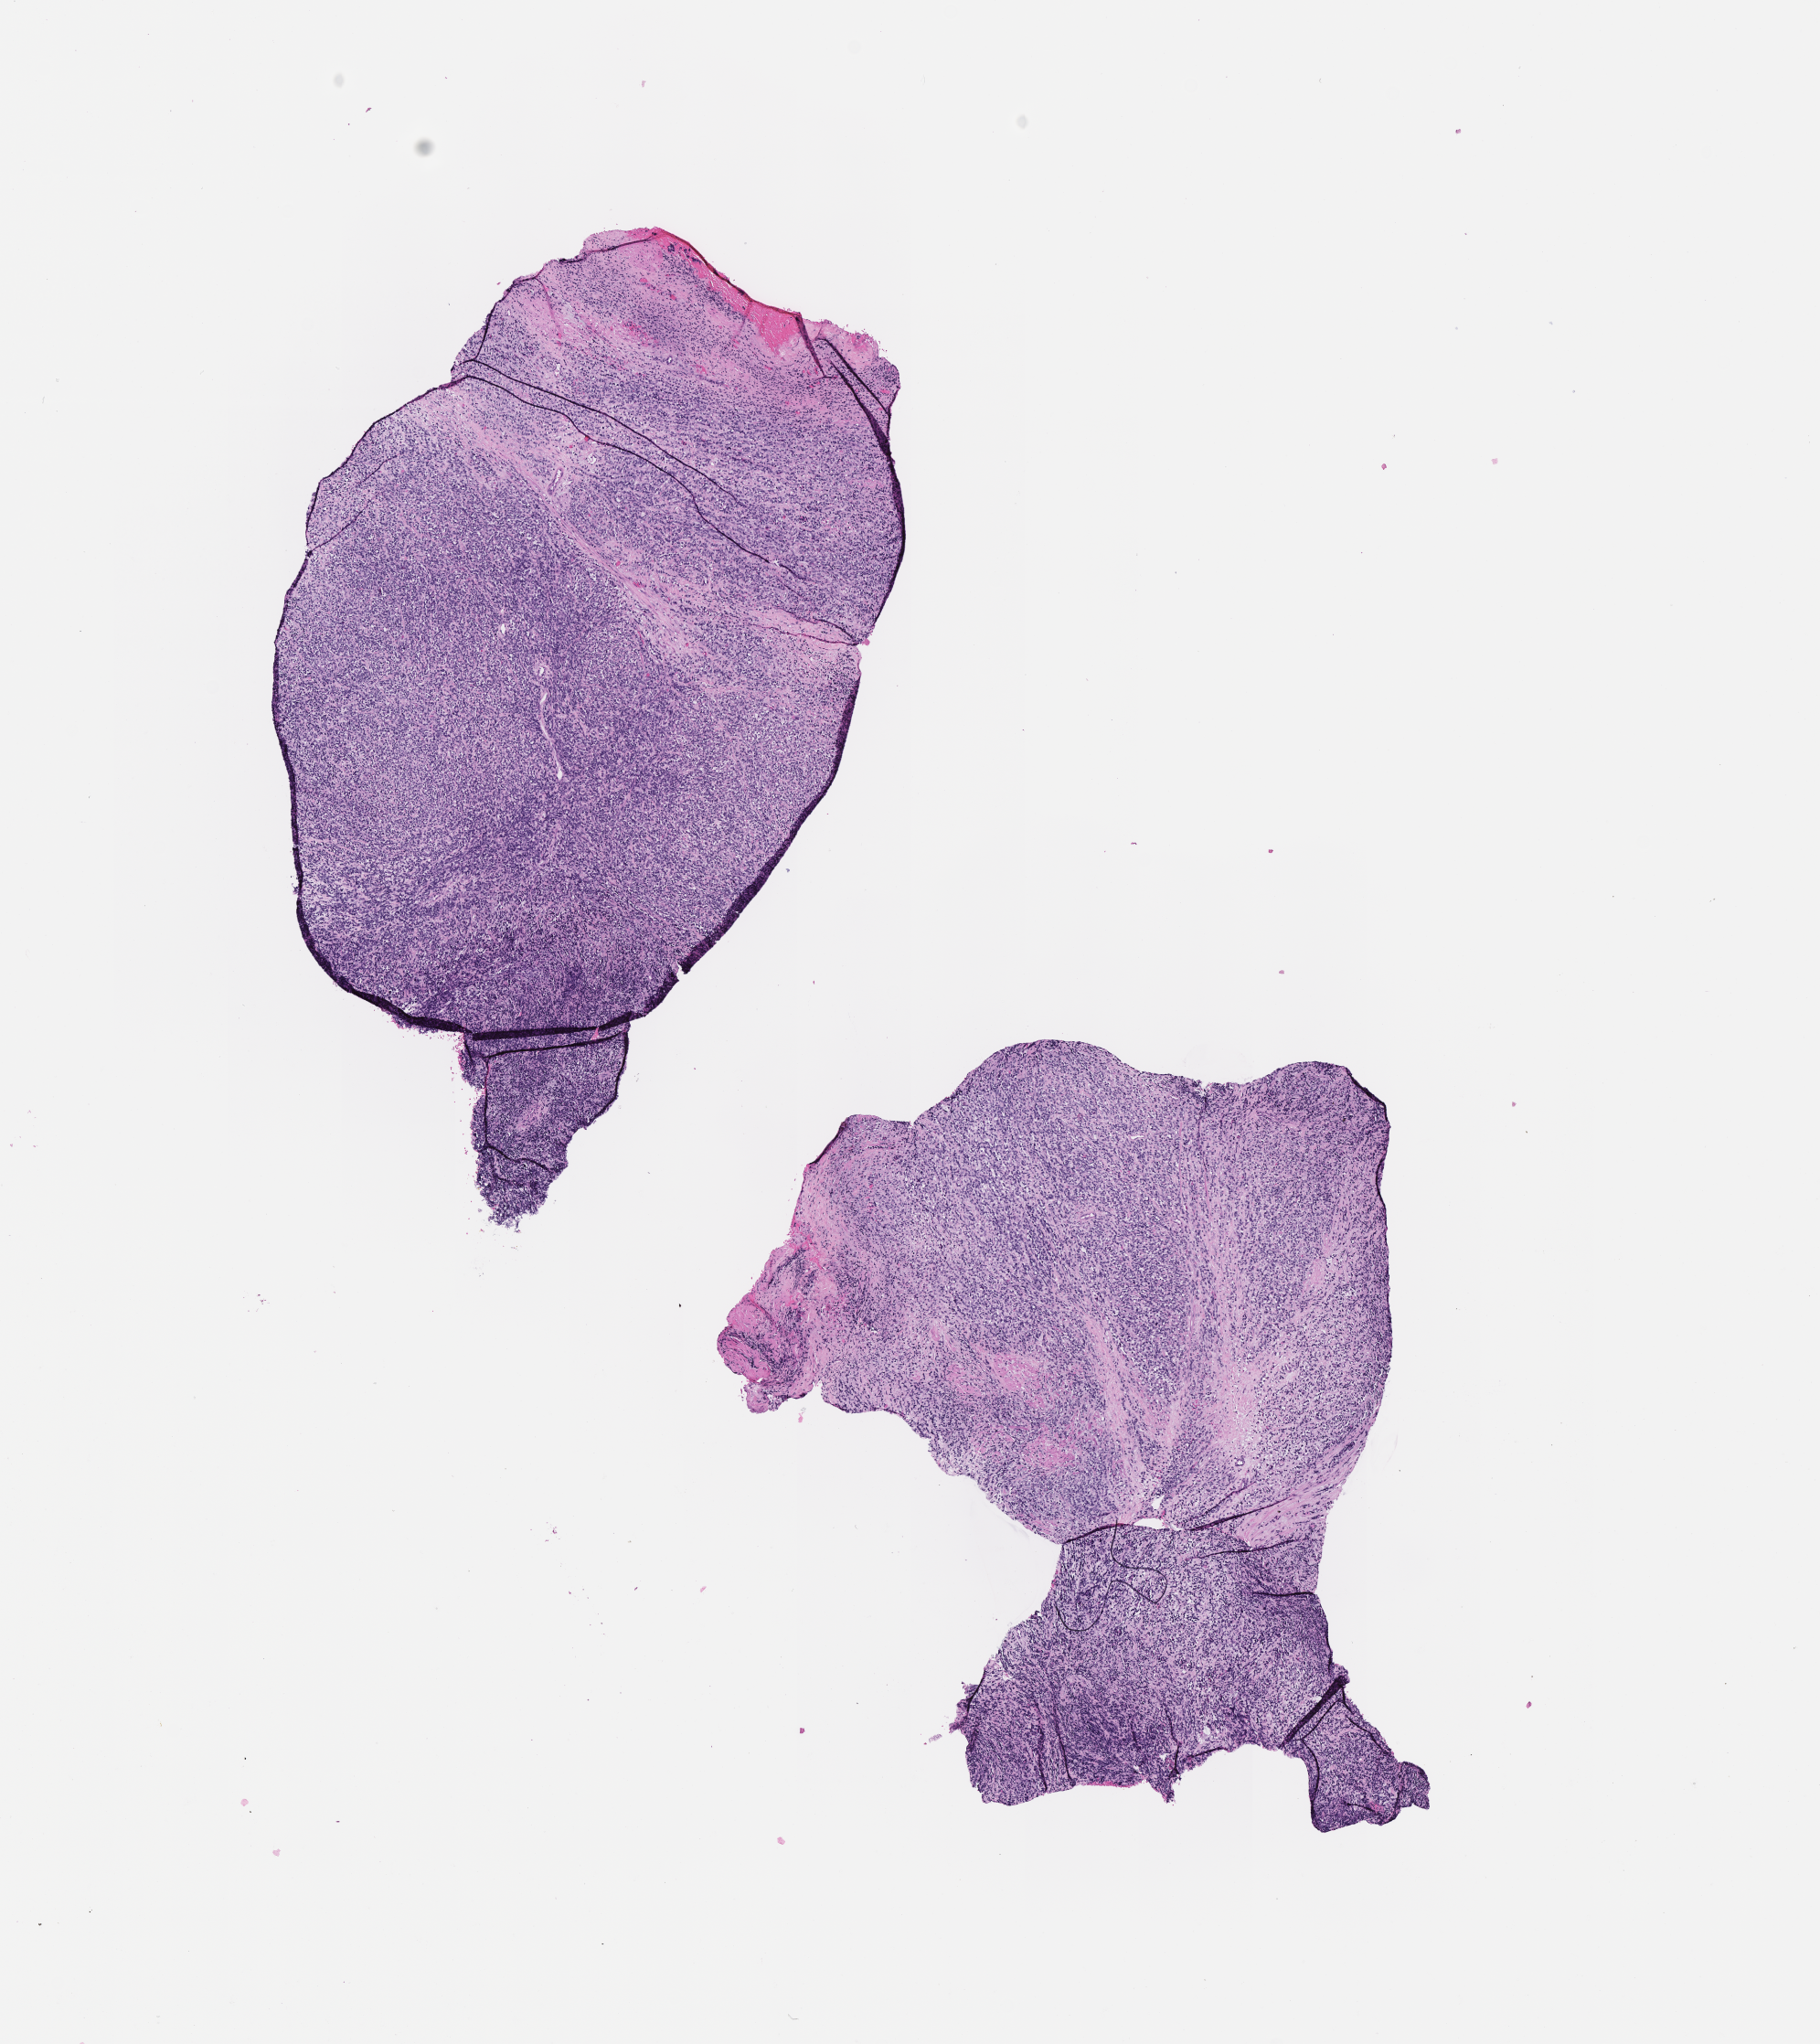
Digitized haematoxylin and eosin-stained section of tumor tissue, whole scanned area (about 8.1 x 9.0 mm) shown as a low-resolution overview; formalin-fixed paraffin-embedded section. Patient: male, age 1.3 years at diagnosis.
Diagnosis: rhabdomyosarcoma; histological classification: embryonal rhabdomyosarcoma. Stage (as recorded): 3. Metastatic status at presentation (as recorded): non-metastatic.